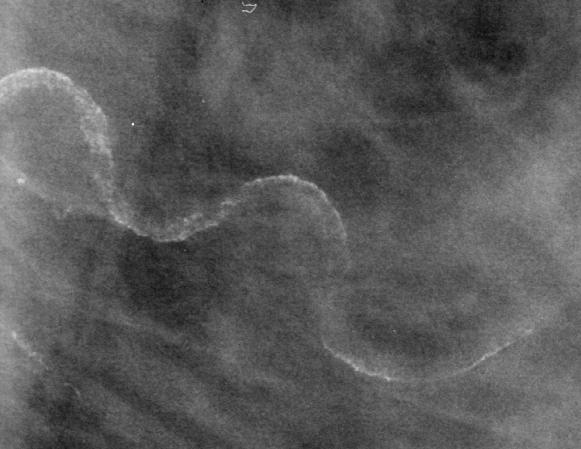
Region of interest cut from a scanned film mammogram (one marked finding), left breast, MLO view, BI-RADS breast density category 4 (scale 1–4).
- Finding: calcifications, morphology vascular; BI-RADS assessment category 2; benign; no additional work-up was recommended (benign without callback).